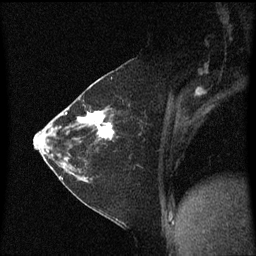
Breast MRI (dynamic contrast-enhanced), one sagittal slice. Dynamic contrast-enhanced series, image 2 of 3 at this slice position (ordered by acquisition). 1.5 T. TE 4.2 ms, TR 8.4 ms. 2 mm slice thickness. 256 × 256 image matrix, field of view 200 × 200 mm. Patient: female, 36 years. Case-level facts recorded for this patient, not image findings: setting: breast cancer imaged before/during neoadjuvant chemotherapy; receptor status: HR-positive, HER2-negative.
Annotated regions visible in this slice (semi-automatically segmented with operator editing):
- analysis volume of interest (the breast-tissue region the enhancement analysis was run in; not a lesion): bounding box [x1, y1, x2, y2] px = [66, 102, 119, 179]
- tumour enhancement mask (voxels above the 70 % enhancement threshold inside the analysis volume of interest): [66, 110, 115, 139]